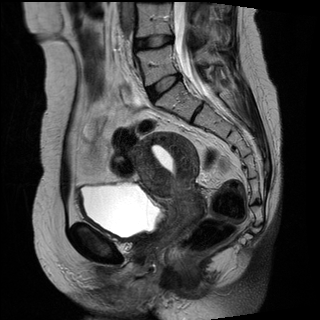
Pelvic MRI for cervical cancer, one sagittal slice. Position 13 of 27 along the scan axis. T2-weighted. 1.5 T. TE 89 ms, TR 2740 ms. 320 × 320 image matrix, field of view 260 × 260 mm. Female patient, age 42 years.
Annotated regions visible in this slice (outlined manually by an expert reader):
- uterus and cervix: bounding box [x1, y1, x2, y2] px = [131, 131, 203, 242]